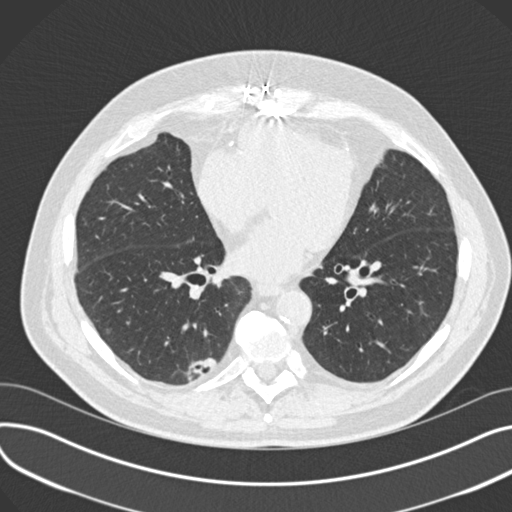
Low-dose screening chest CT, one axial slice; position 76 of 177 along the scan axis; reconstruction kernel B30f; lung window (W 1500 / L -600 HU); 2 mm slice thickness; 512 × 512 image matrix, field of view 372 × 372 mm.
Annotated regions visible in this slice (expert manual segmentation):
- lesion 1 (tumor, lower lobe of right lung): bounding box [x1, y1, x2, y2] px = [185, 358, 219, 381]